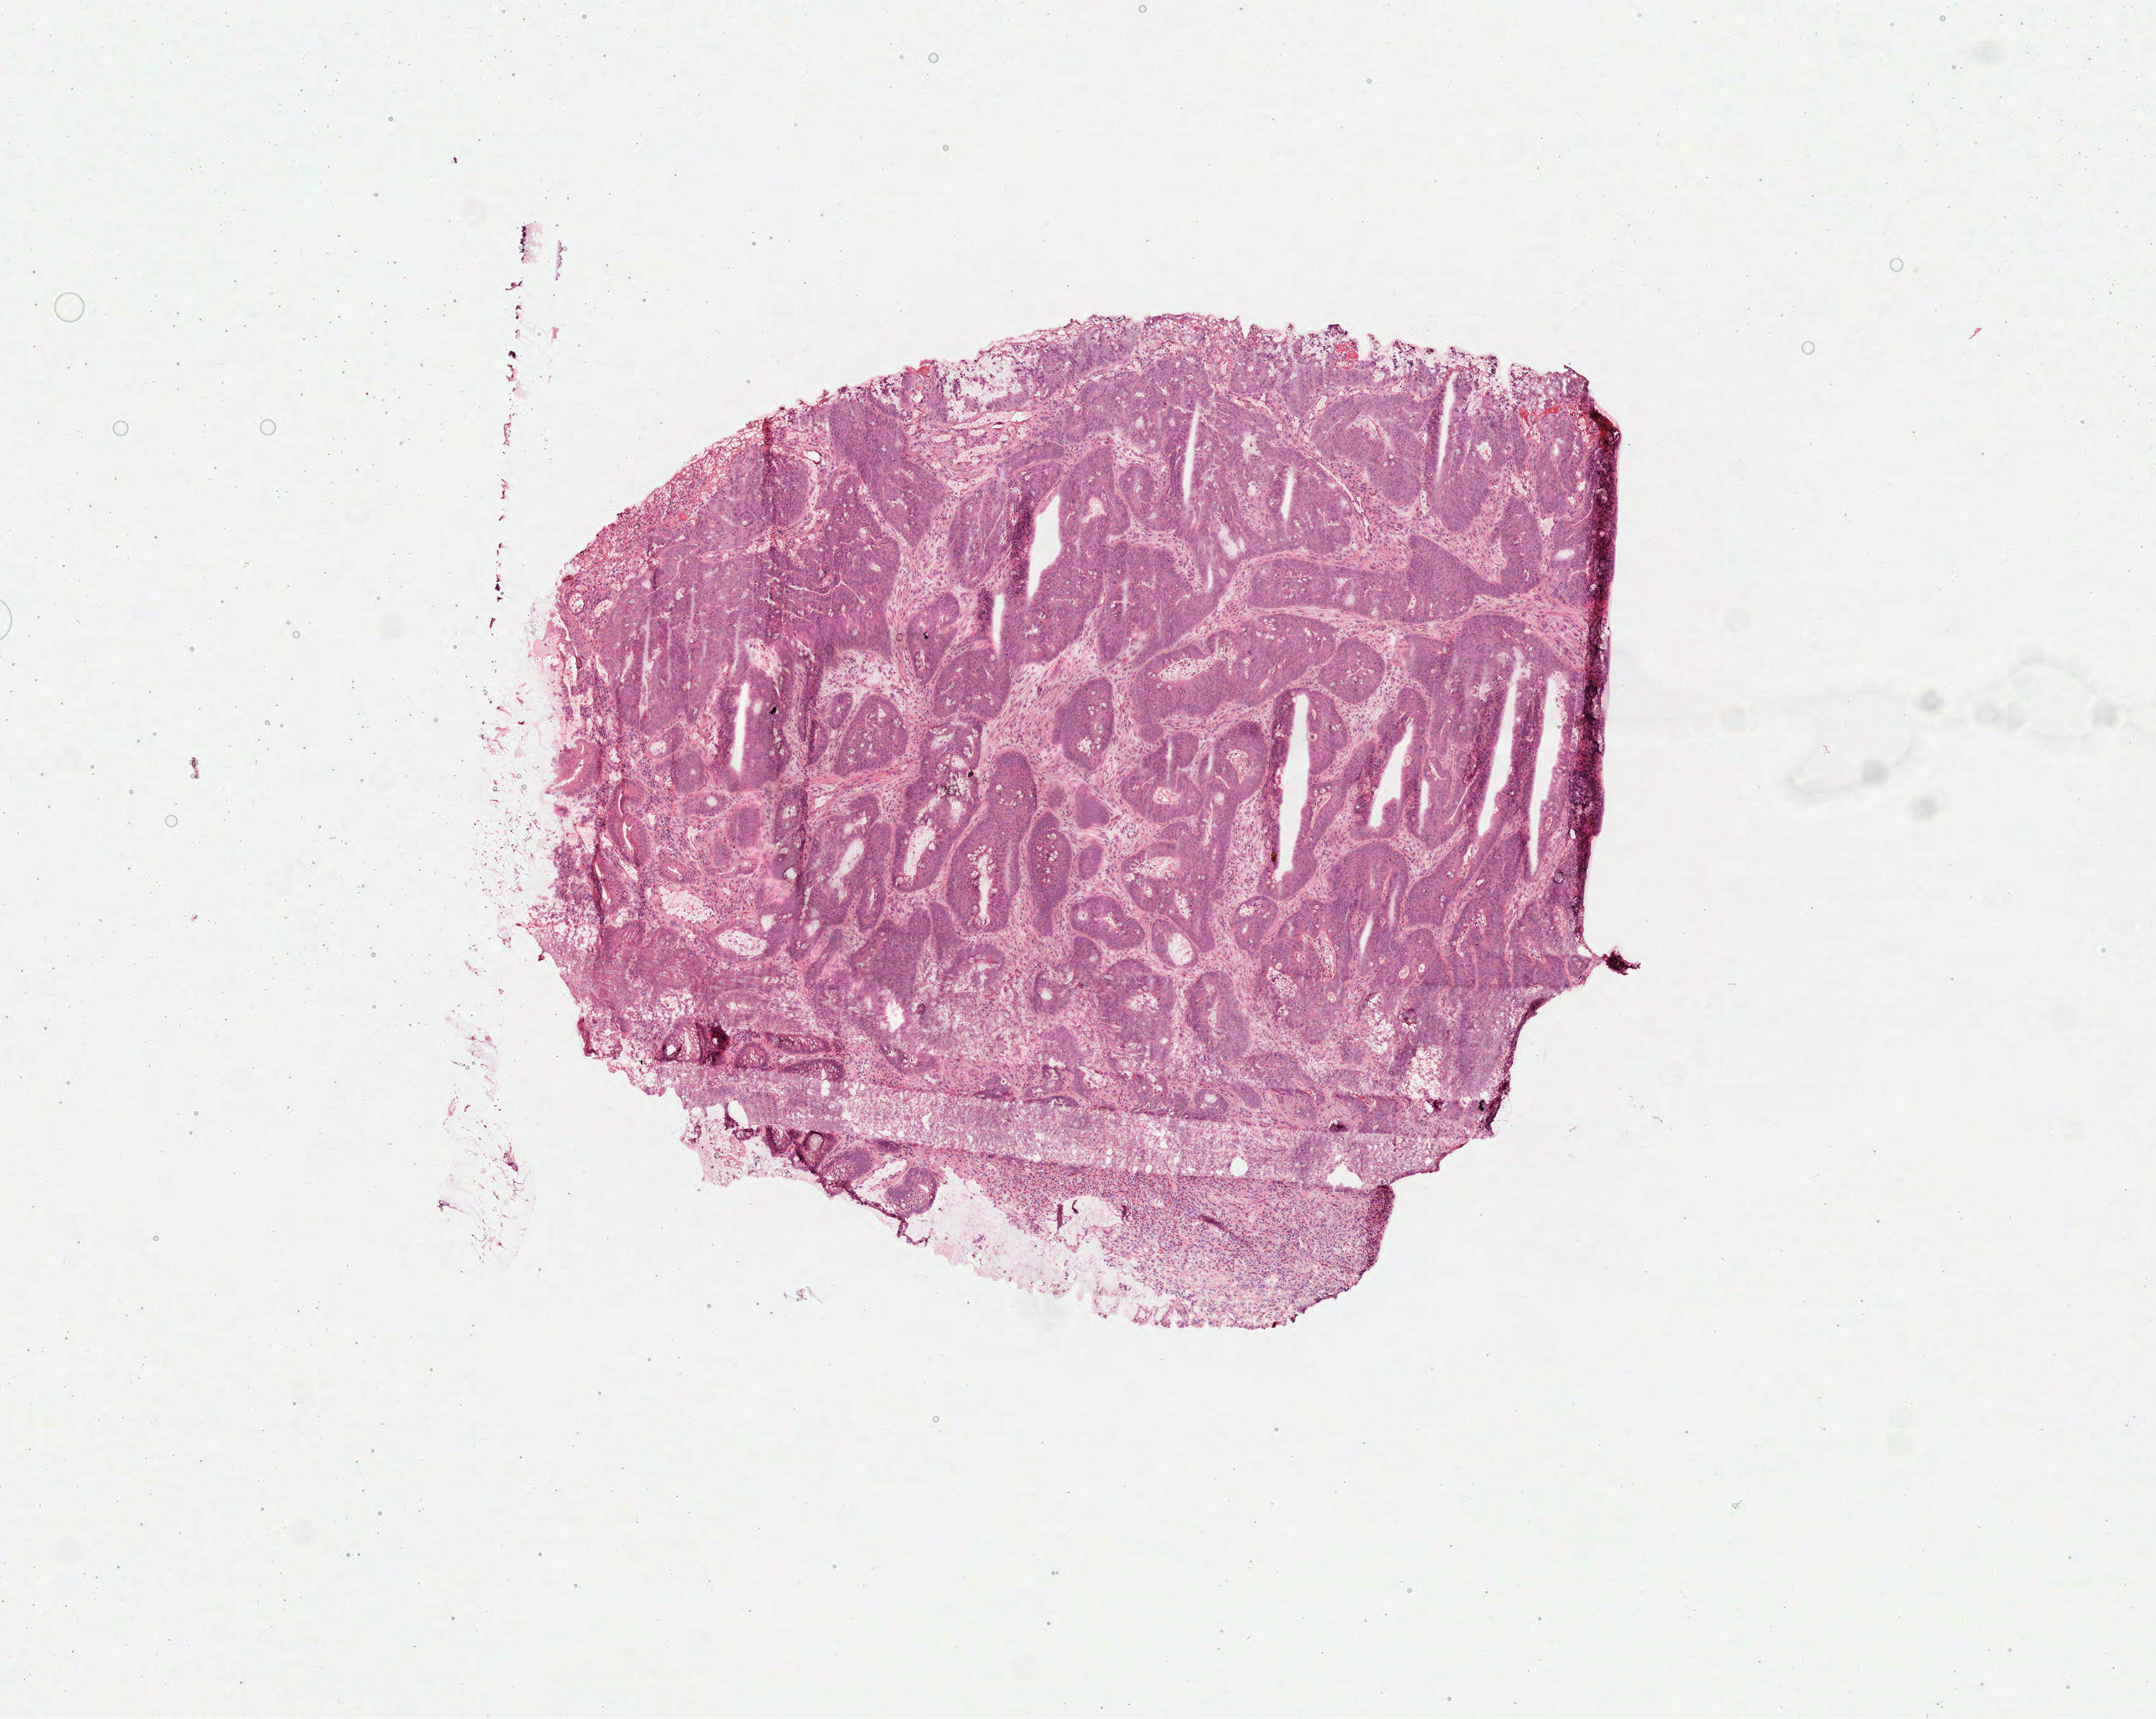
Digitized Hematoxylin and eosin (H&E) stained tissue section (whole slide), a low-resolution overview of the entire scanned area, about 7.0 x 5.6 mm (slide scanned at 40x); frozen section from the top of the tissue portion; sample: primary tumour, colon. Female patient; age at initial diagnosis 76 years. Slide review estimates, as recorded: tumour cells 79%, tumour nuclei 85%, normal cells 0%, stromal cells 20%, necrosis 1%. Inflammatory infiltration, as recorded: lymphocyte infiltration 3%, monocyte infiltration 0%, neutrophil infiltration 1%.
Diagnosis: Adenocarcinoma, NOS (sigmoid colon). AJCC pathologic stage: IIA (7th edition). Lymph nodes positive (case pathology): 0 of 5 examined.